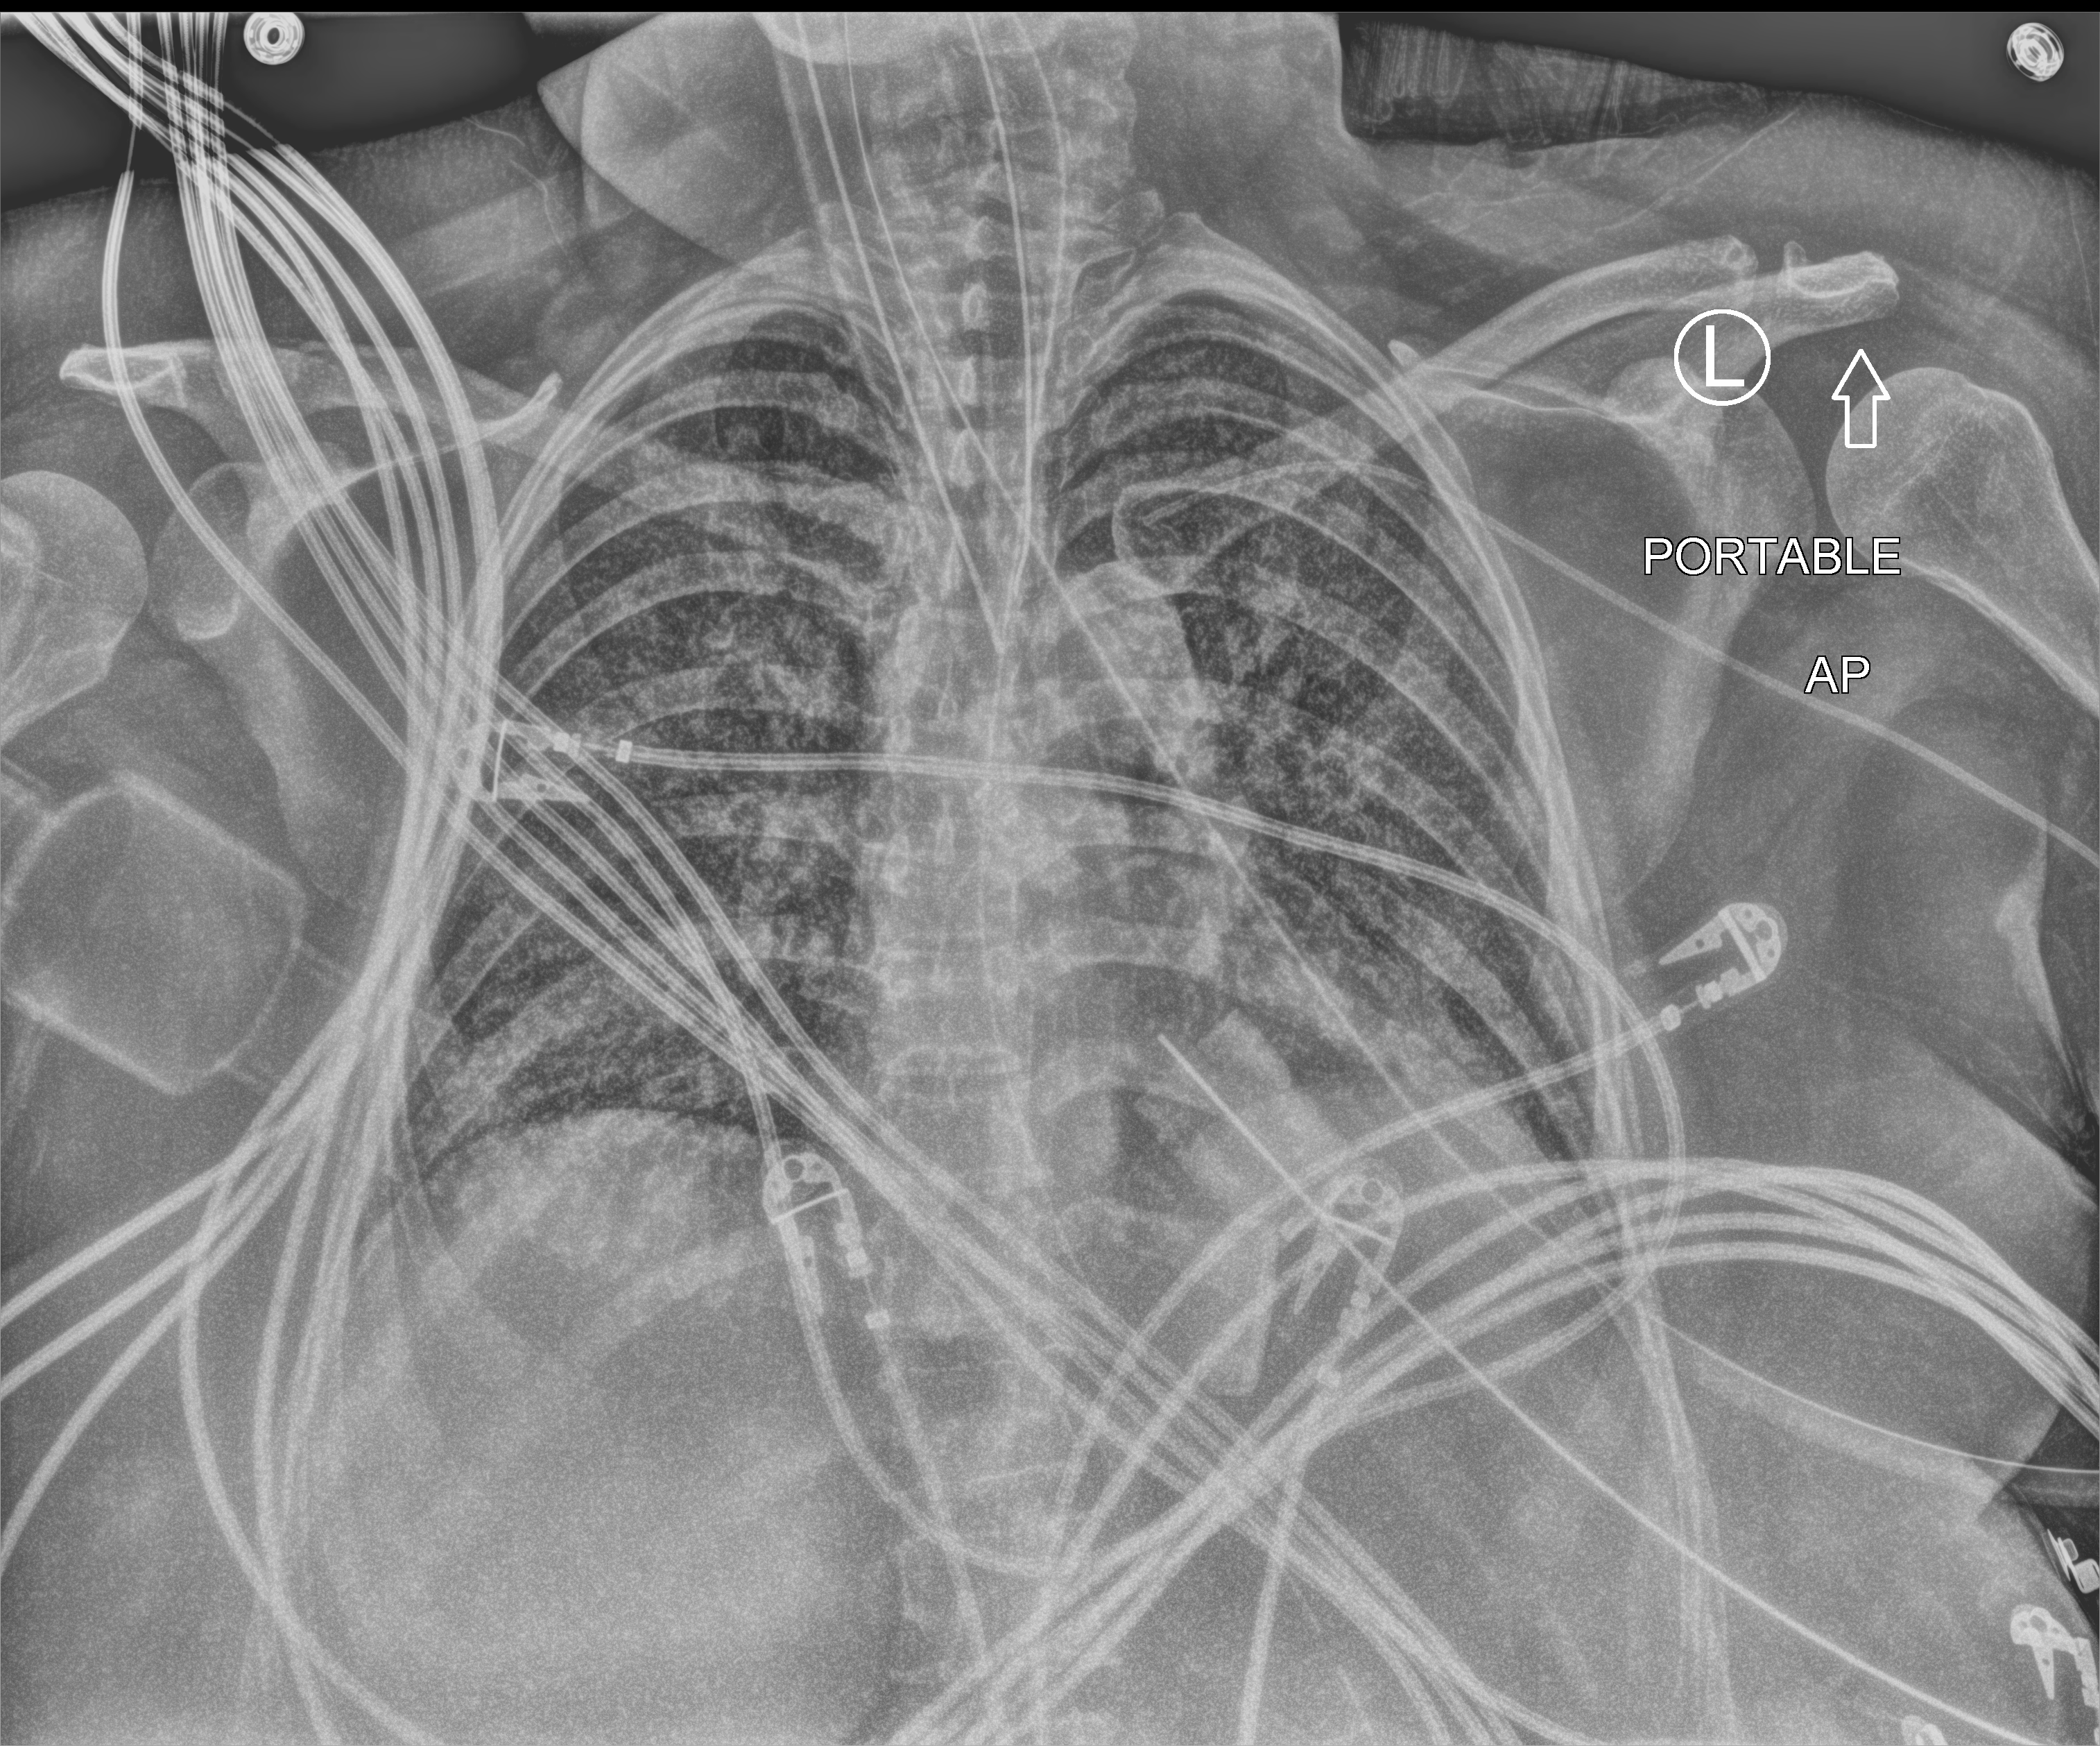
Portable chest radiograph, anteroposterior (AP) projection. Female patient hospitalised with COVID-19, age 18–59 years.
Admission-level facts for this patient (not findings on this image; timing relative to this image not recorded):
- smoking status (admission record): never